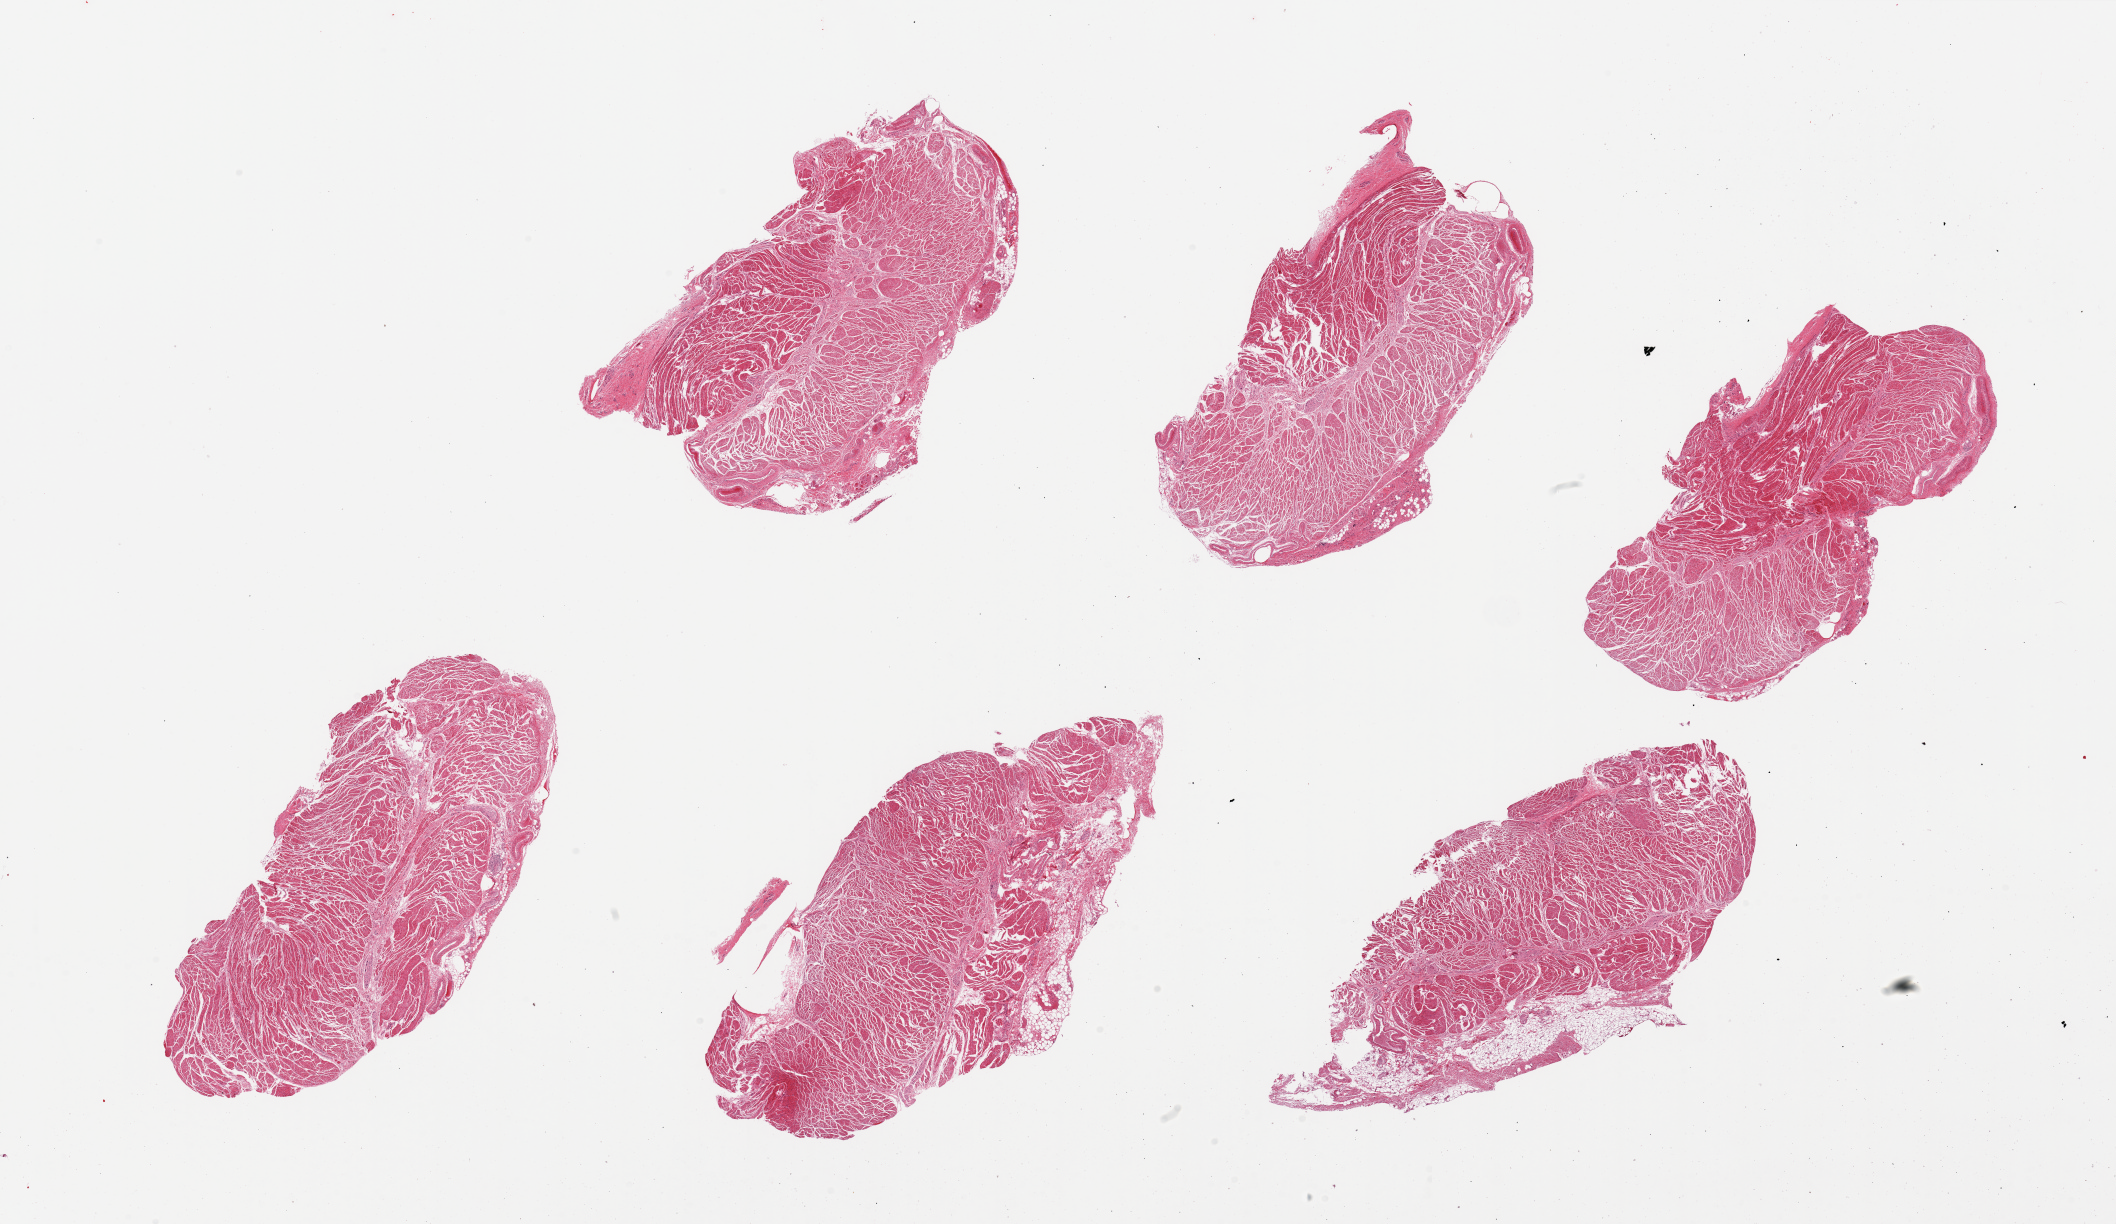
Whole-slide image, hematoxylin and eosin (H&E) stain, brightfield, a low-resolution overview of the entire scanned area, about 33.5 x 19.4 mm. PAXgene-fixed, paraffin-embedded tissue. Sampled site (target tissue): gastroesophageal junction. Donor tissue sample. Donor: male.
Review note (as recorded): 6 pieces.